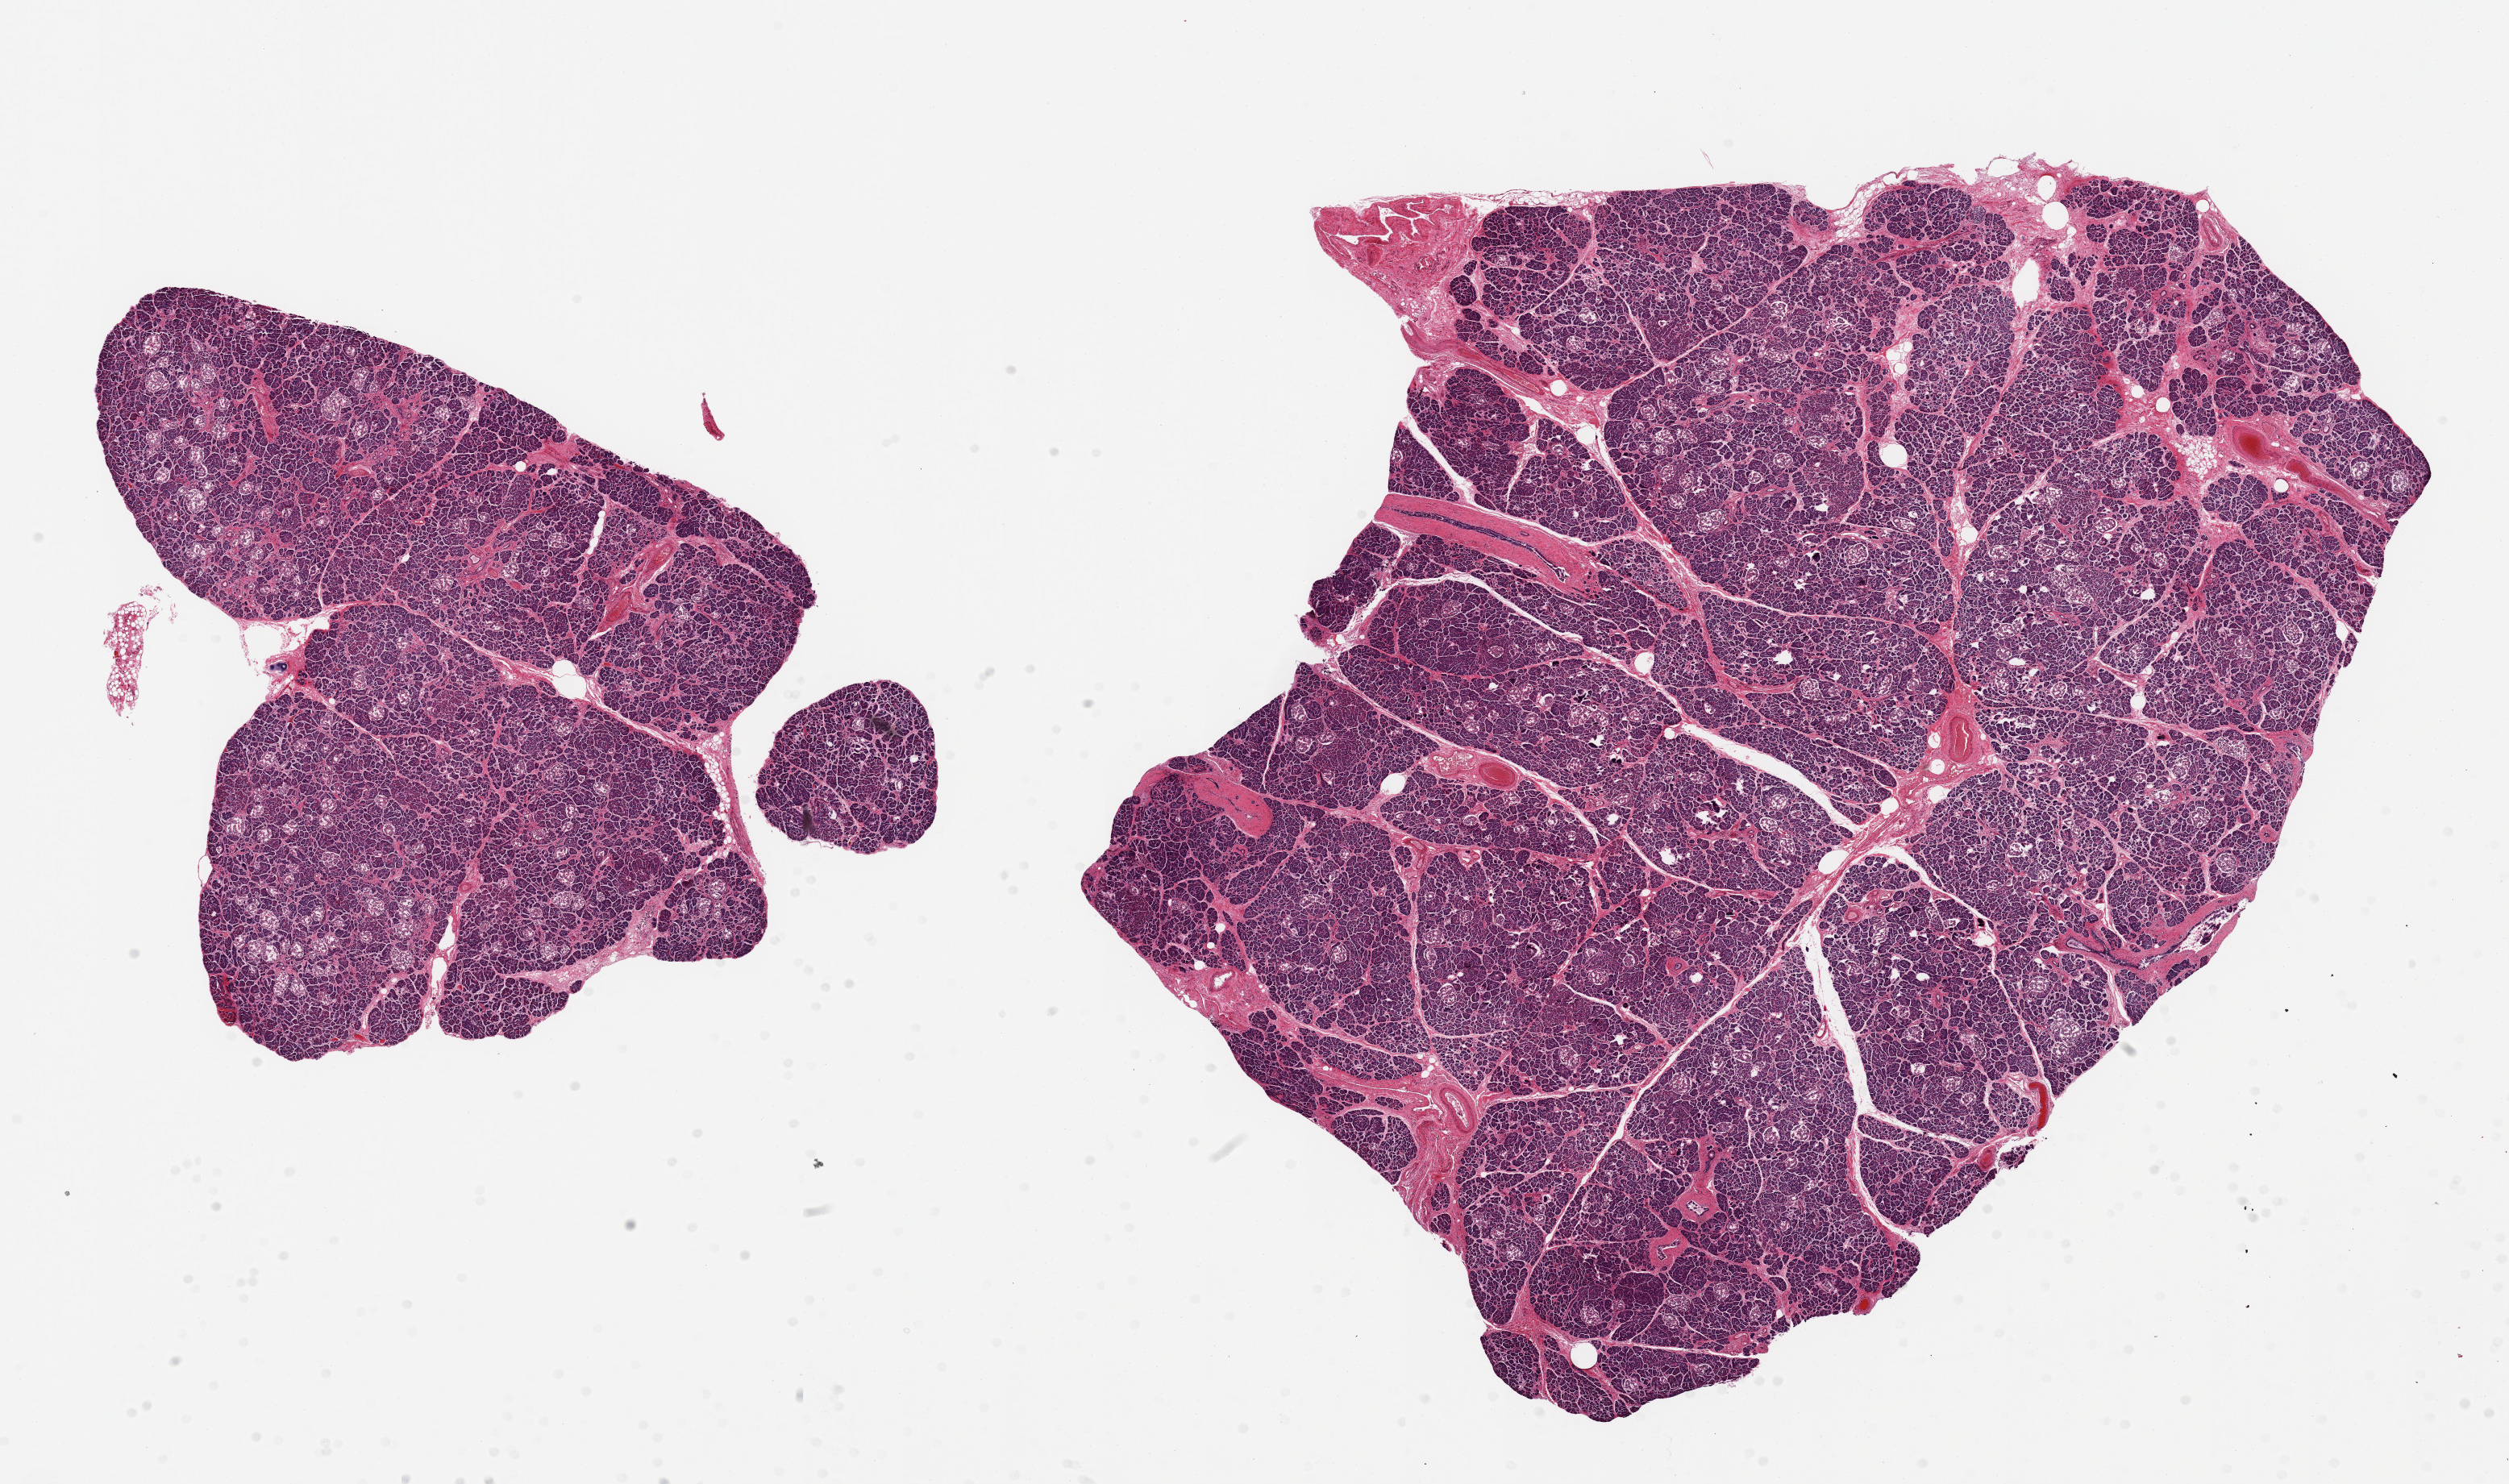
Whole-slide image, H&E stain — low-resolution overview of the scanned area, about 24.6 x 14.6 mm (acquisition: 20x scan). PAXgene-fixed, paraffin-embedded tissue. Sampled site (target tissue): pancreas. Donor tissue sample. Donor: male.
Reviewer comment on this tissue sample: 2 pieces, mild saponification; islets numerous and well preserved.